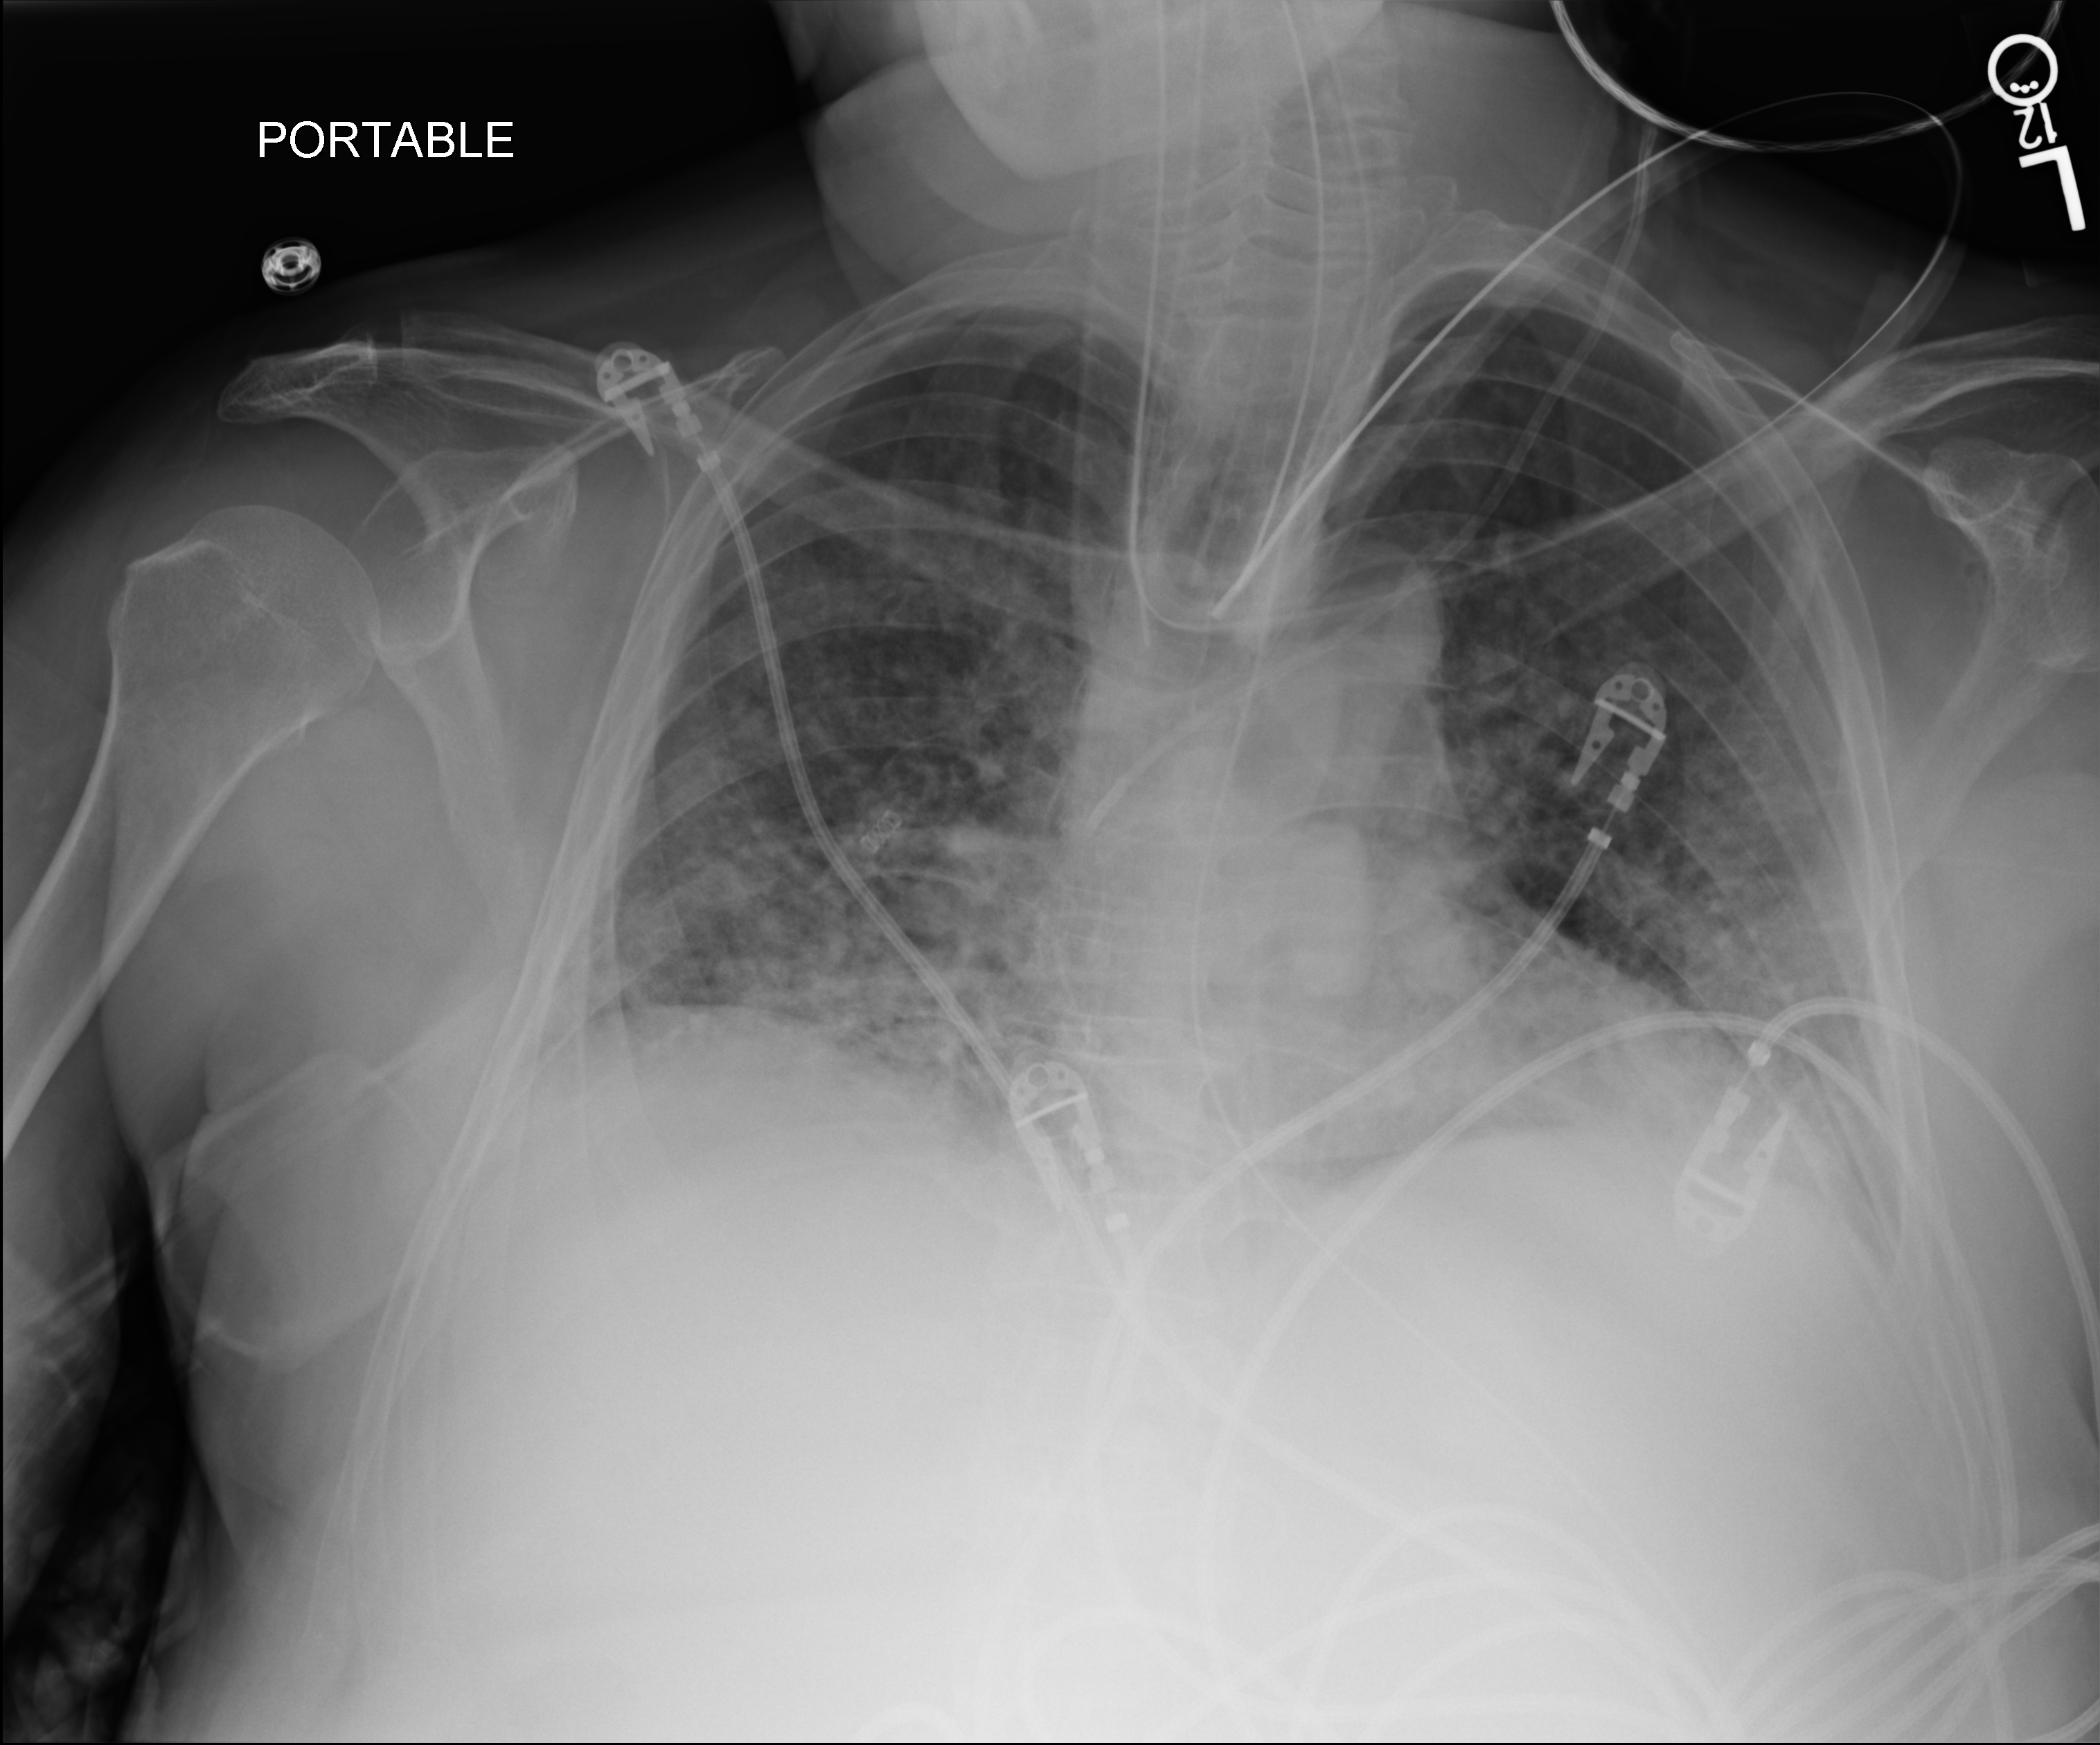
Portable chest radiograph; anteroposterior (AP) projection. Patient hospitalised with COVID-19; male, aged 60–74 years.
Hospital-stay facts (about this admission, not read from this image; timing relative to this image not recorded): admitted to intensive care during this hospital stay: yes.